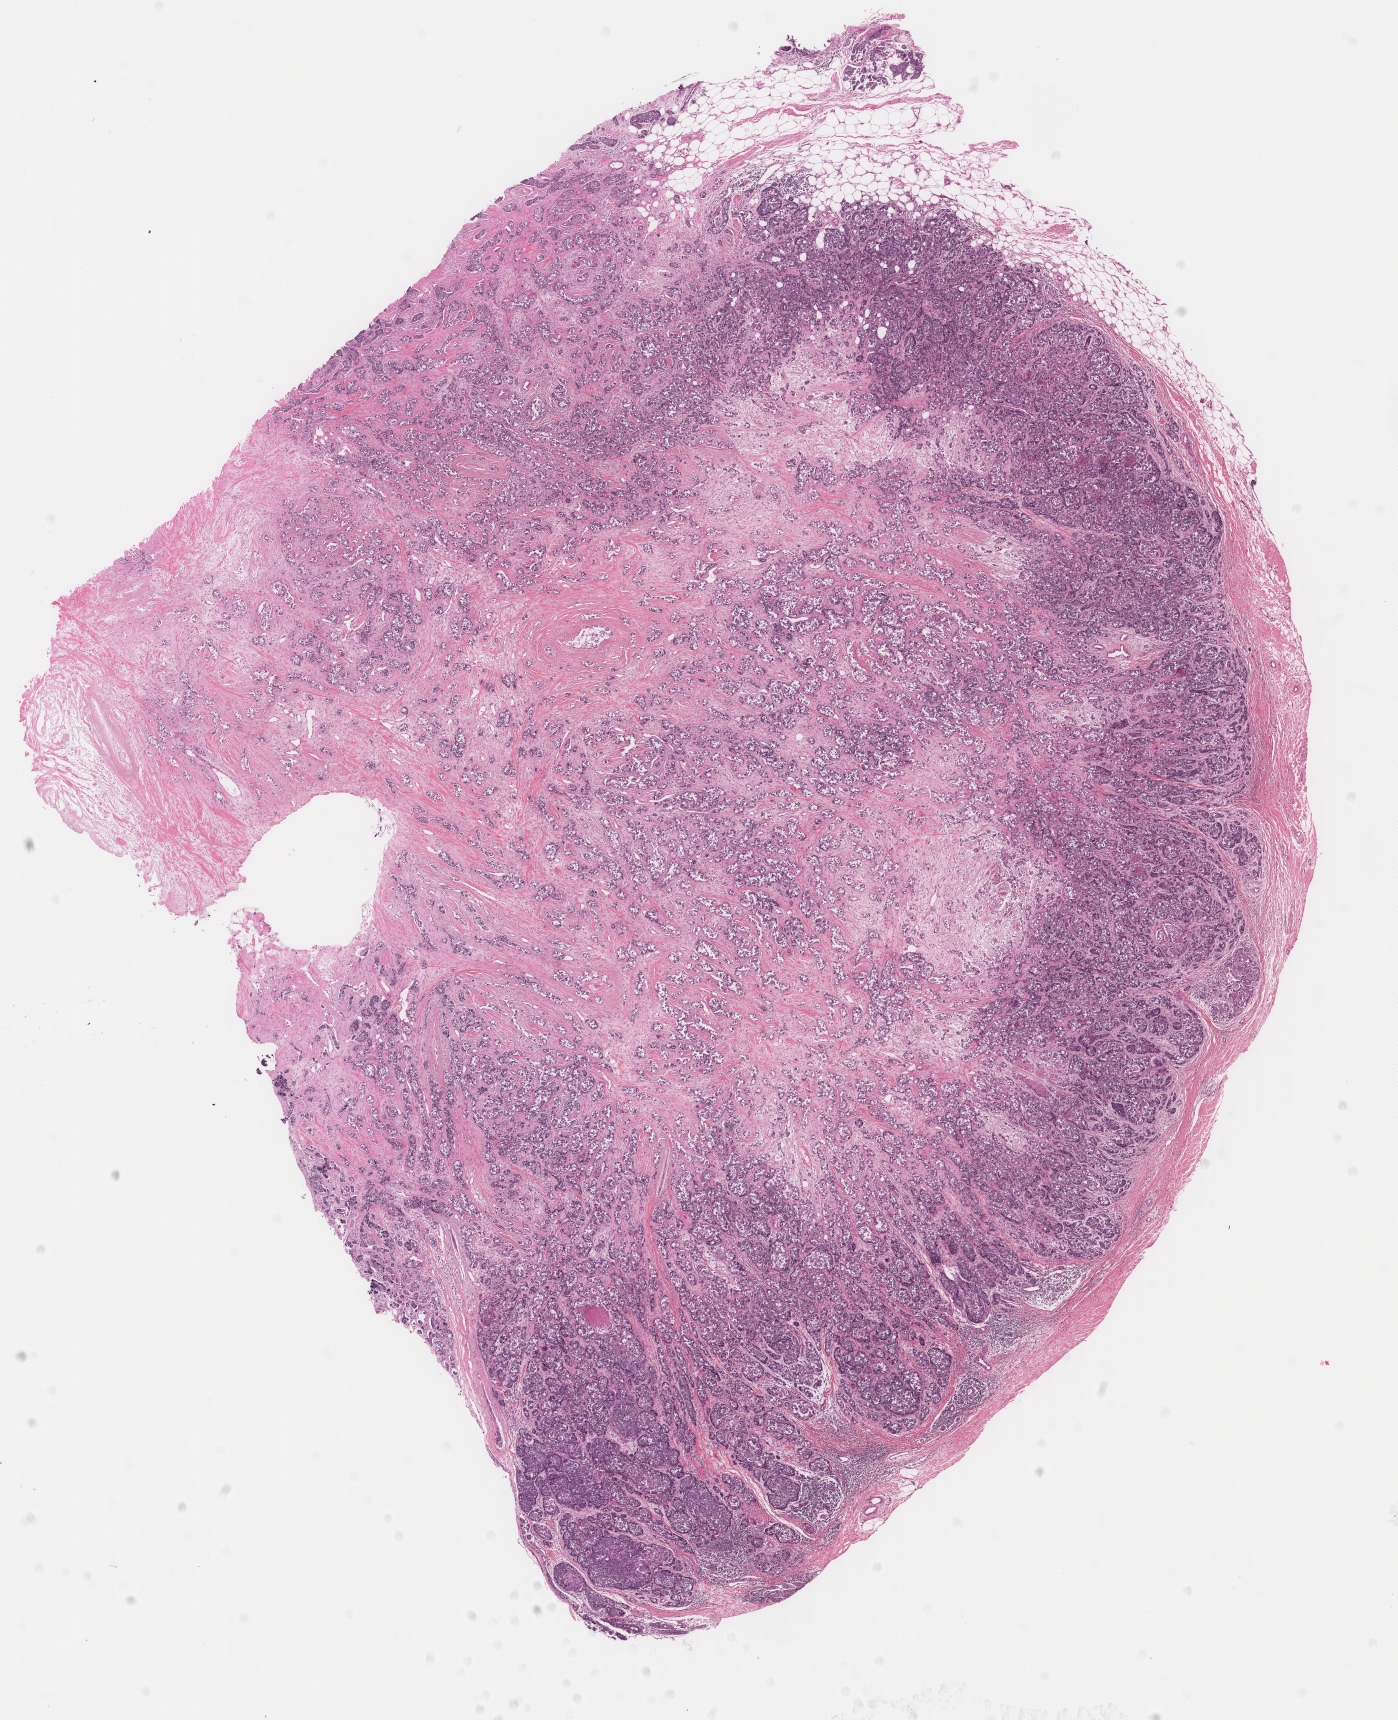
H&E-stained whole-slide image, a low-resolution overview of the entire scanned area, about 11.1 x 13.7 mm (acquisition: 40x scan); formalin-fixed paraffin-embedded (FFPE) diagnostic section; breast, primary tumour sample. Female, age 52 years at initial diagnosis.
Diagnosis: Infiltrating duct carcinoma, NOS. AJCC pathologic stage: IIA. TNM: T2 N0 M0.